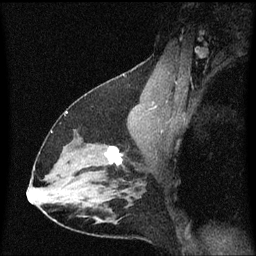
Breast MRI (dynamic contrast-enhanced), one sagittal slice; position 38 of 60 along the scan axis; dynamic contrast-enhanced series, image 2 of 3 at this slice position (ordered by acquisition); 1.5 T; TE 4.2 ms, TR 8.4 ms; 2 mm slice thickness; 256 × 256 image matrix, field of view 200 × 200 mm. Female patient, age 38 years. From the clinical record (not read from this slice): setting: breast cancer imaged before/during neoadjuvant chemotherapy; receptor status: HR-positive, HER2-negative.
Outlined on this slice (semi-automatically segmented with operator editing):
- analysis volume of interest (the breast-tissue region the enhancement analysis was run in; not a lesion): bounding box [x1, y1, x2, y2] px = [94, 138, 141, 185]
- tumour enhancement mask (voxels above the 70 % enhancement threshold inside the analysis volume of interest): [107, 146, 123, 165]